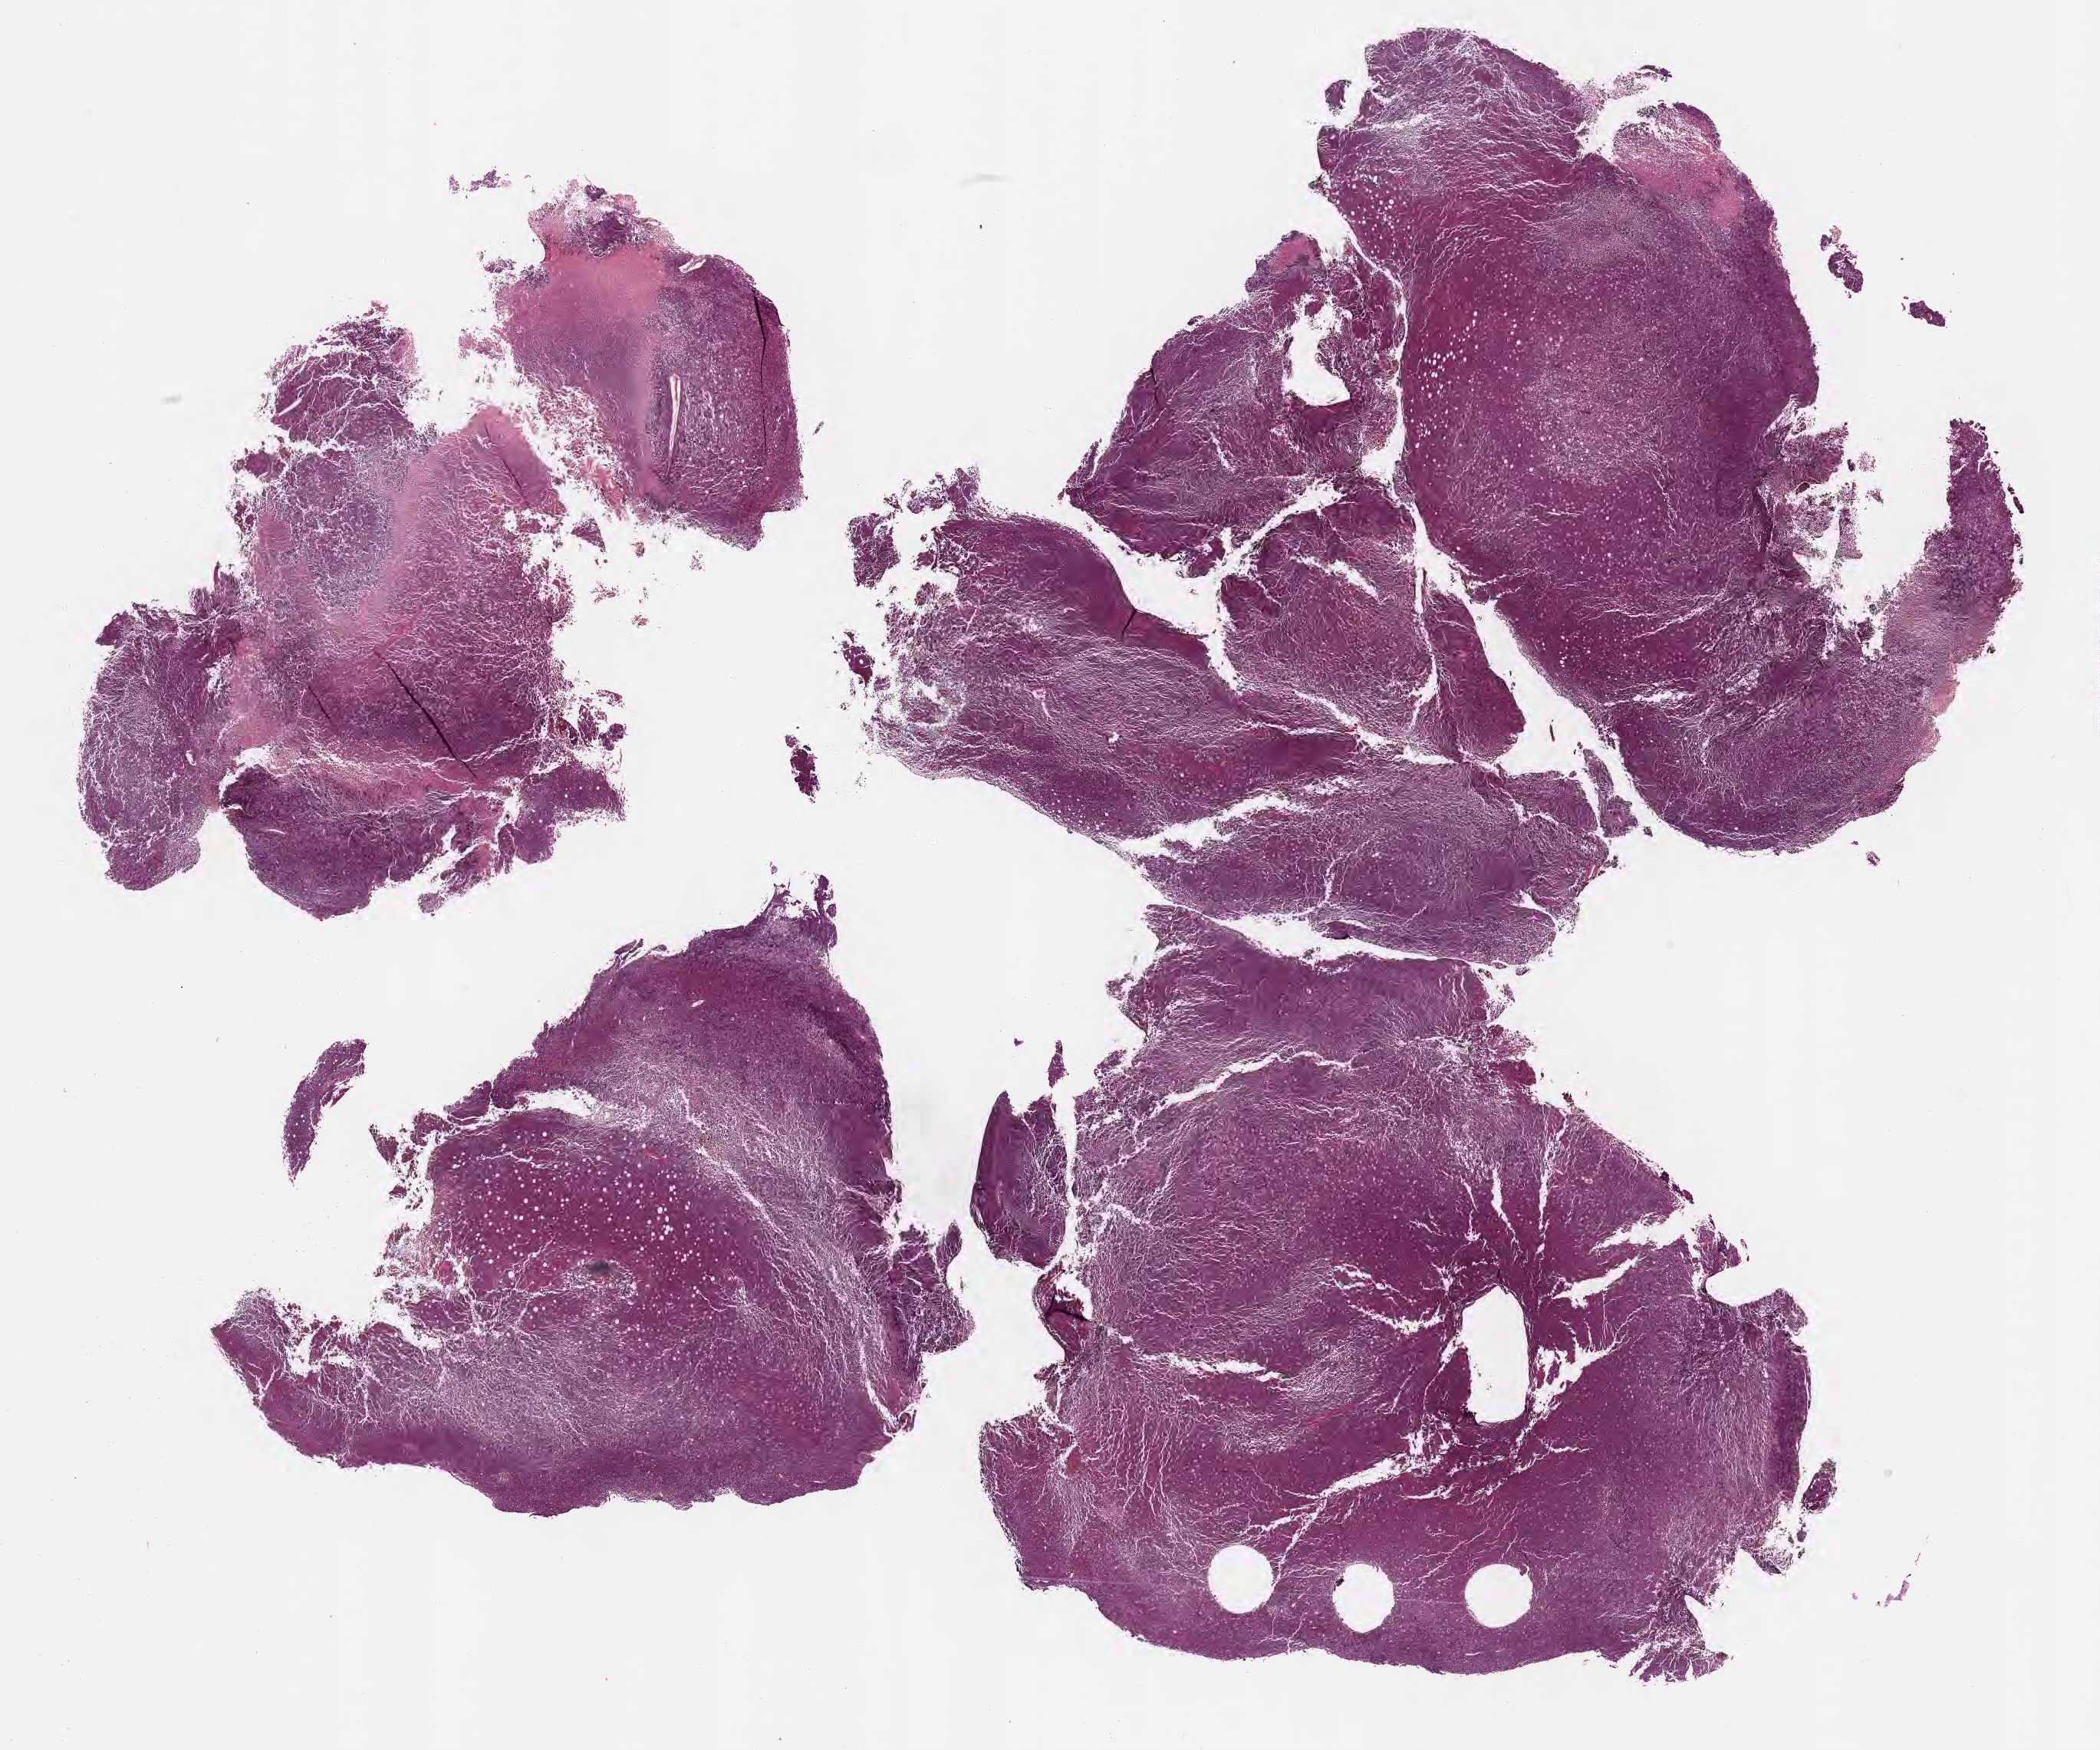
Digitized H&E-stained section, whole scanned area (about 22.1 x 18.5 mm) shown as a low-resolution overview. Formalin-fixed, paraffin-embedded (FFPE) tissue. Specimen: primary tumor. Patient: male, 60 years old.
Diagnosis: Diffuse large B-cell lymphoma, NOS.